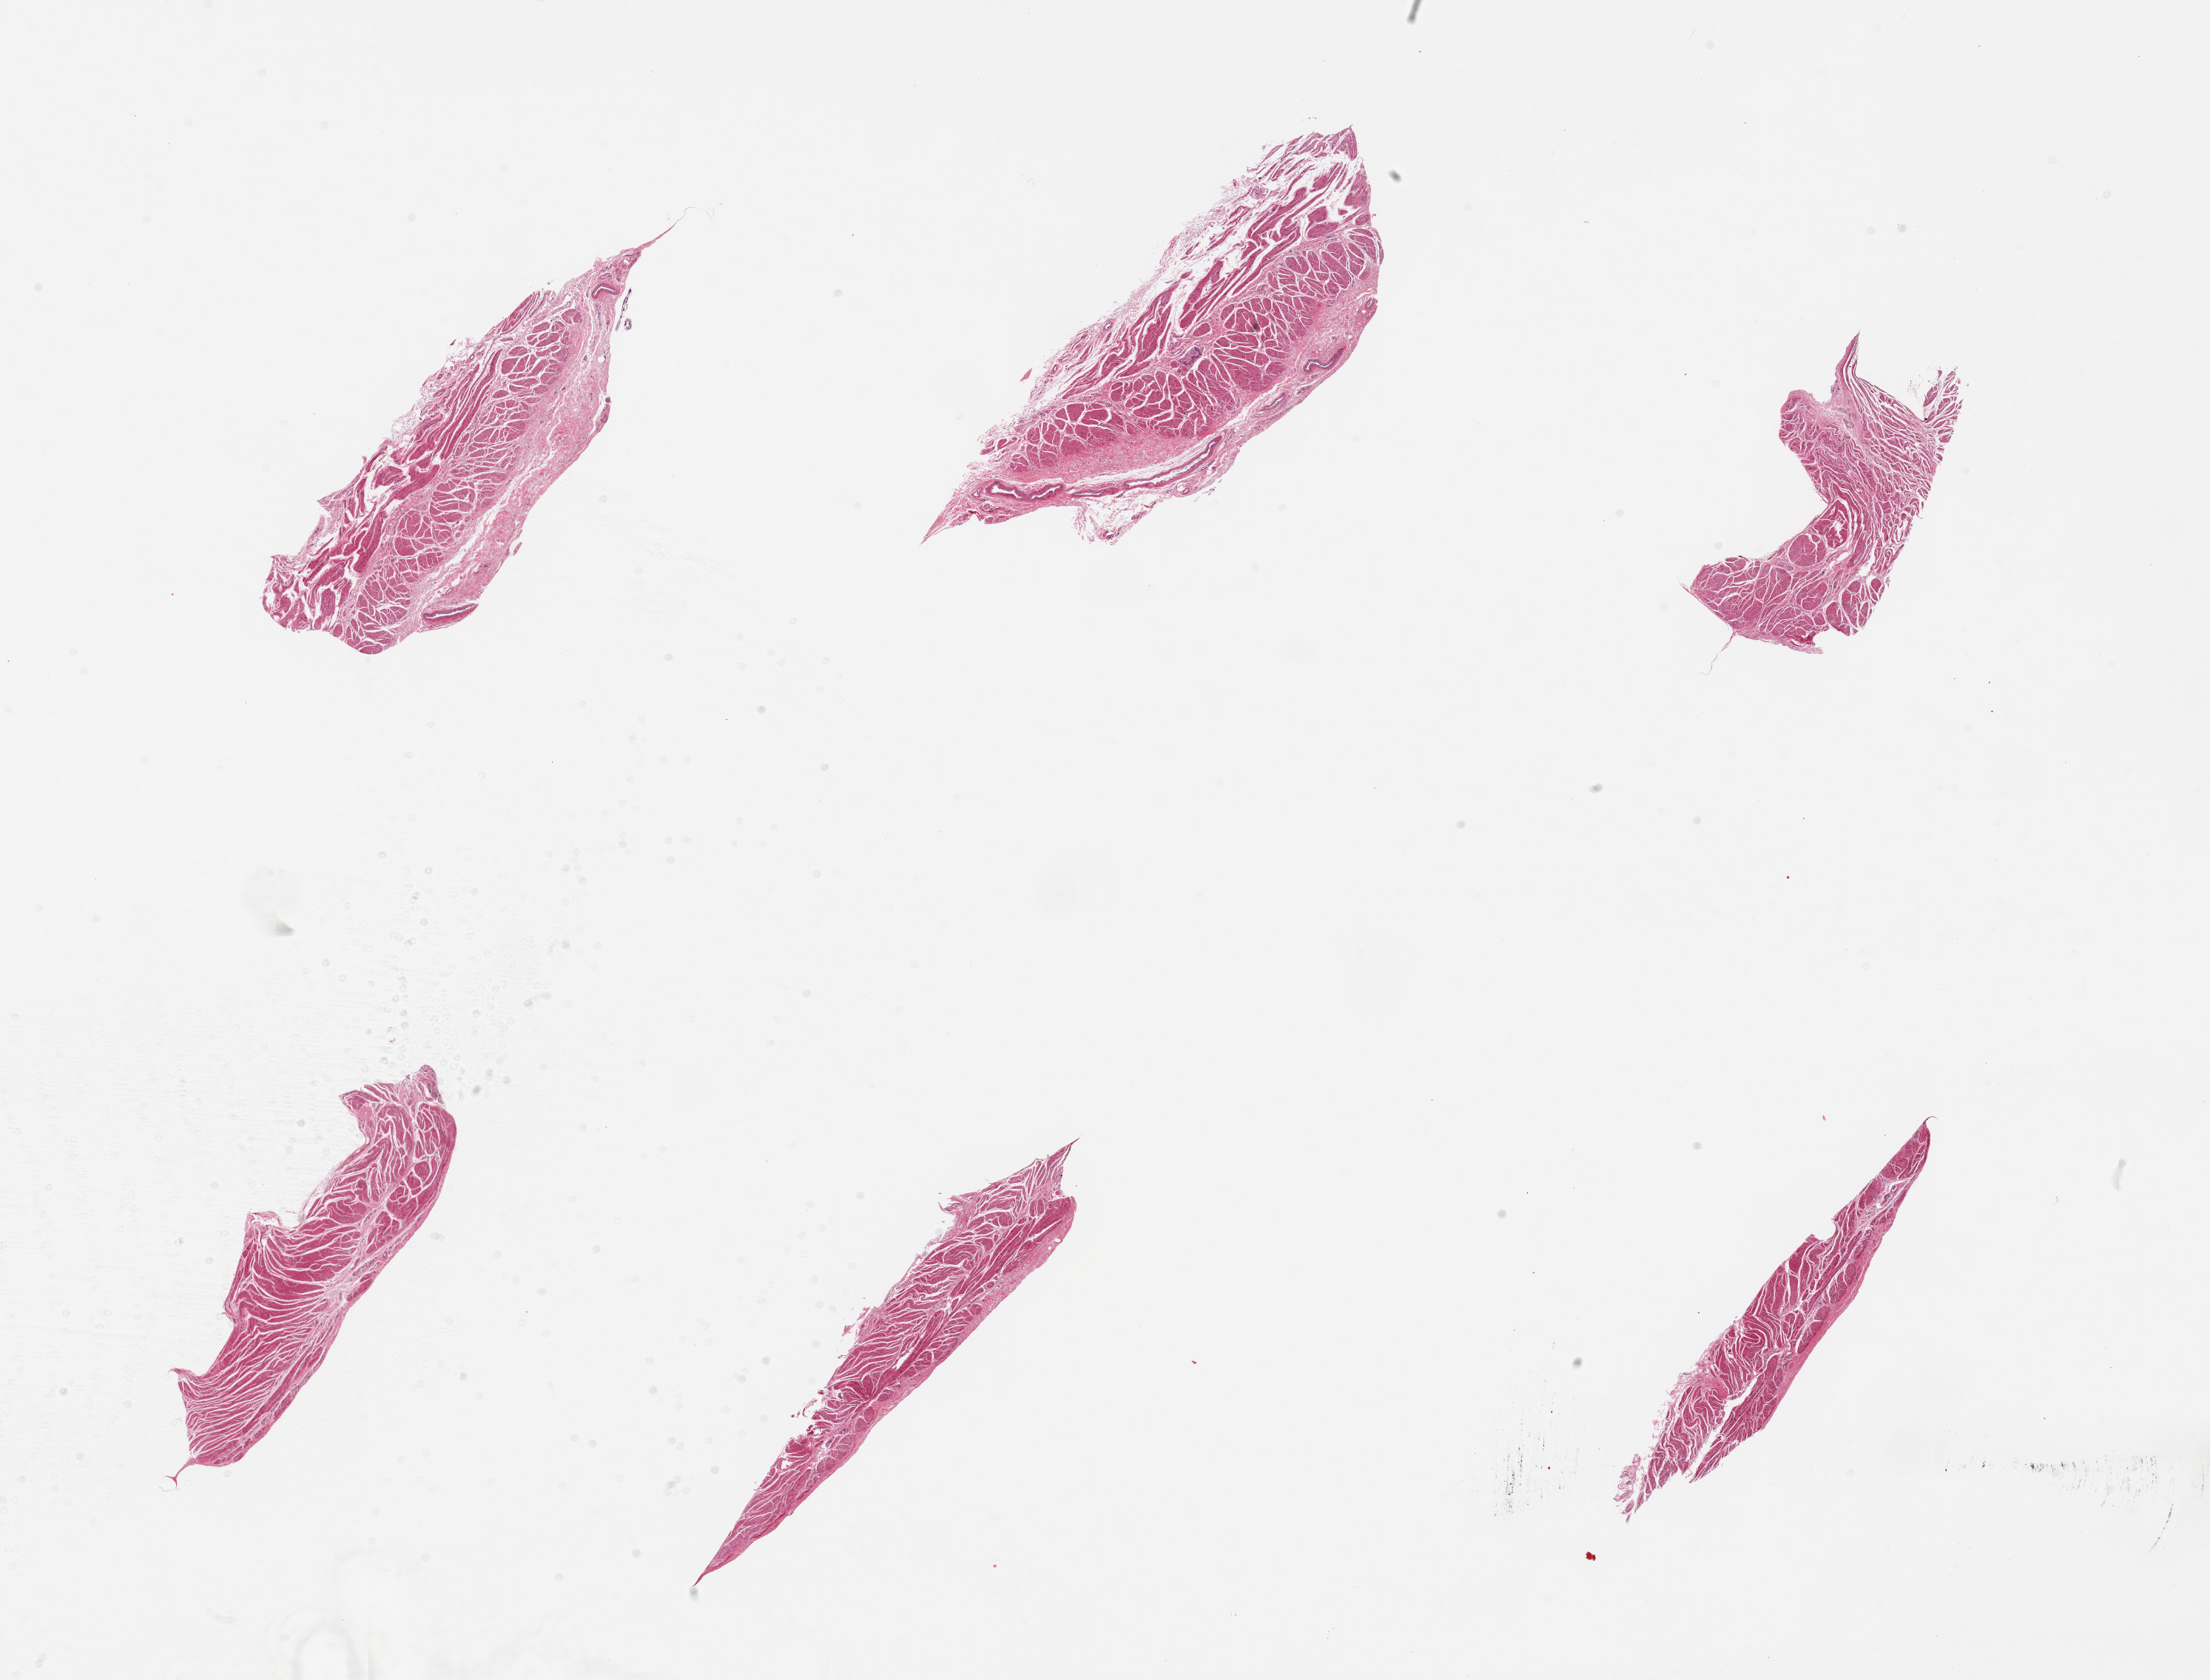
Digitized H&E-stained section — a low-resolution overview of the entire scanned area, about 23.6 x 18.0 mm (slide scanned at 20x), PAXgene-fixed paraffin-embedded (PFPE) section, section of gastroesophageal junction (target tissue), donor tissue sample.
Pathologist's review note for this sample: 6 pieces.